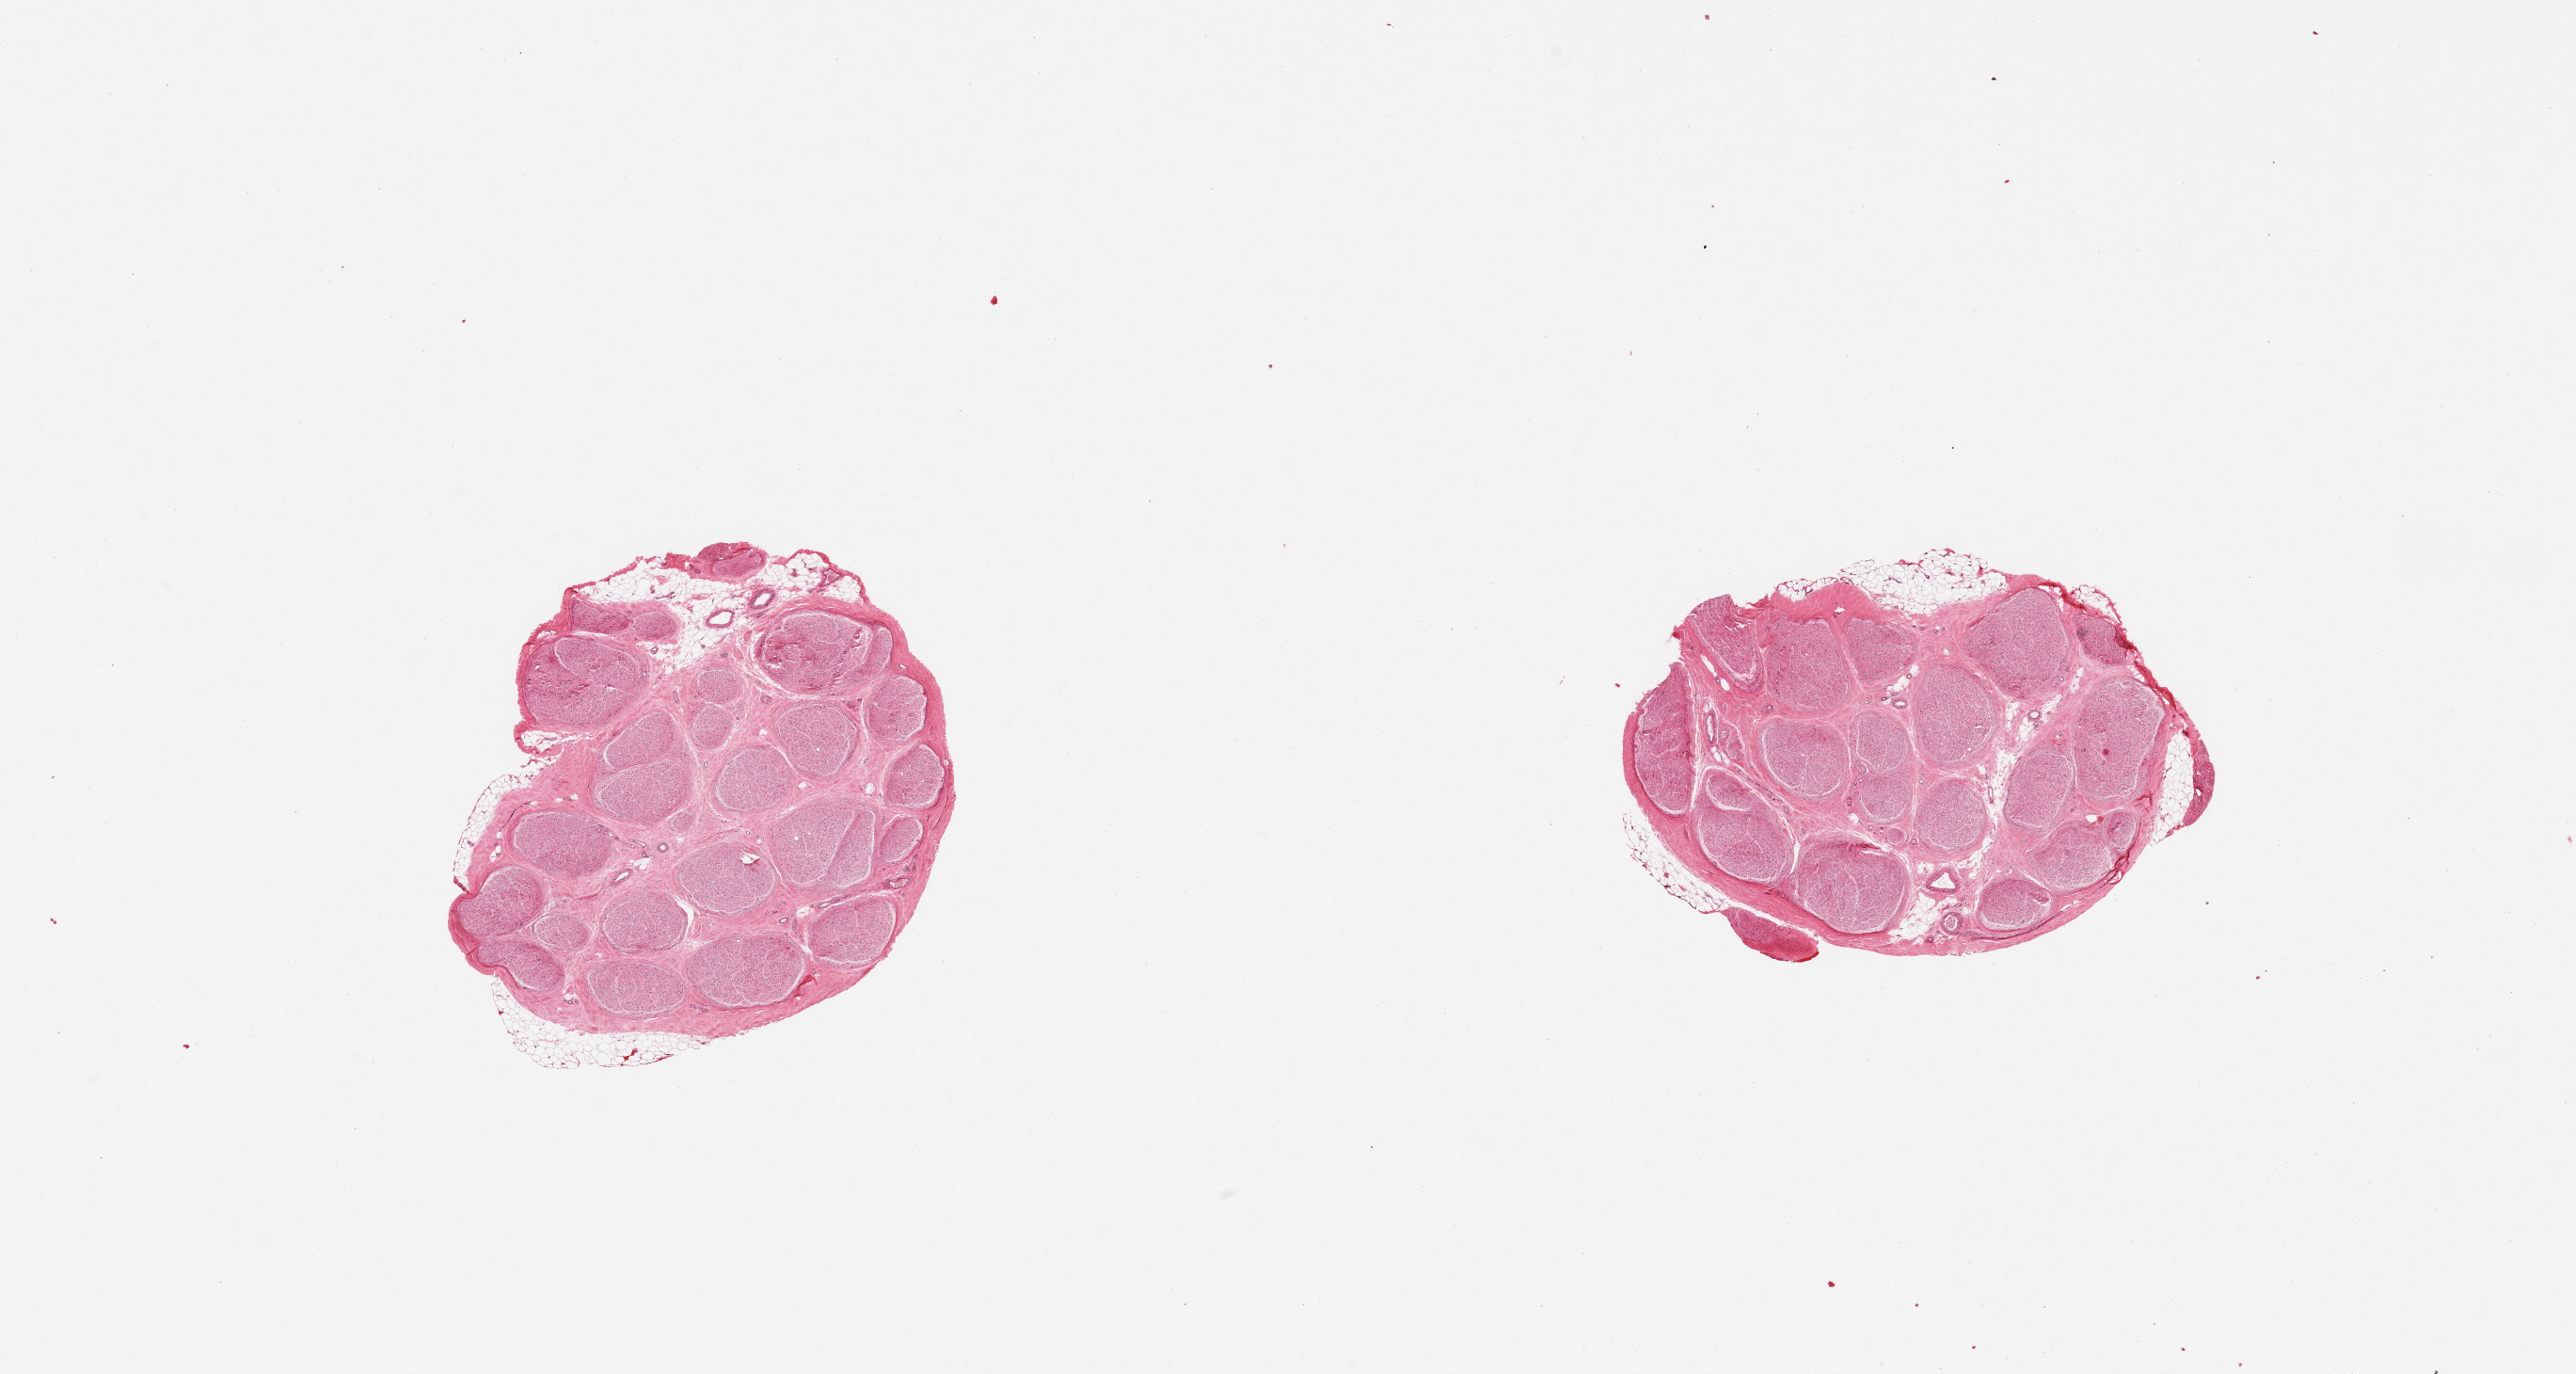
Digitized hematoxylin and eosin (H&E)-stained section — low-resolution overview of the scanned area, about 21.7 x 11.5 mm (from a 20x scan); PAXgene-fixed paraffin-embedded (PFPE) section; section of tibial nerve (target tissue); donor tissue sample. Male donor.
Review note (as recorded): 1 piece; nerve NOT artery.